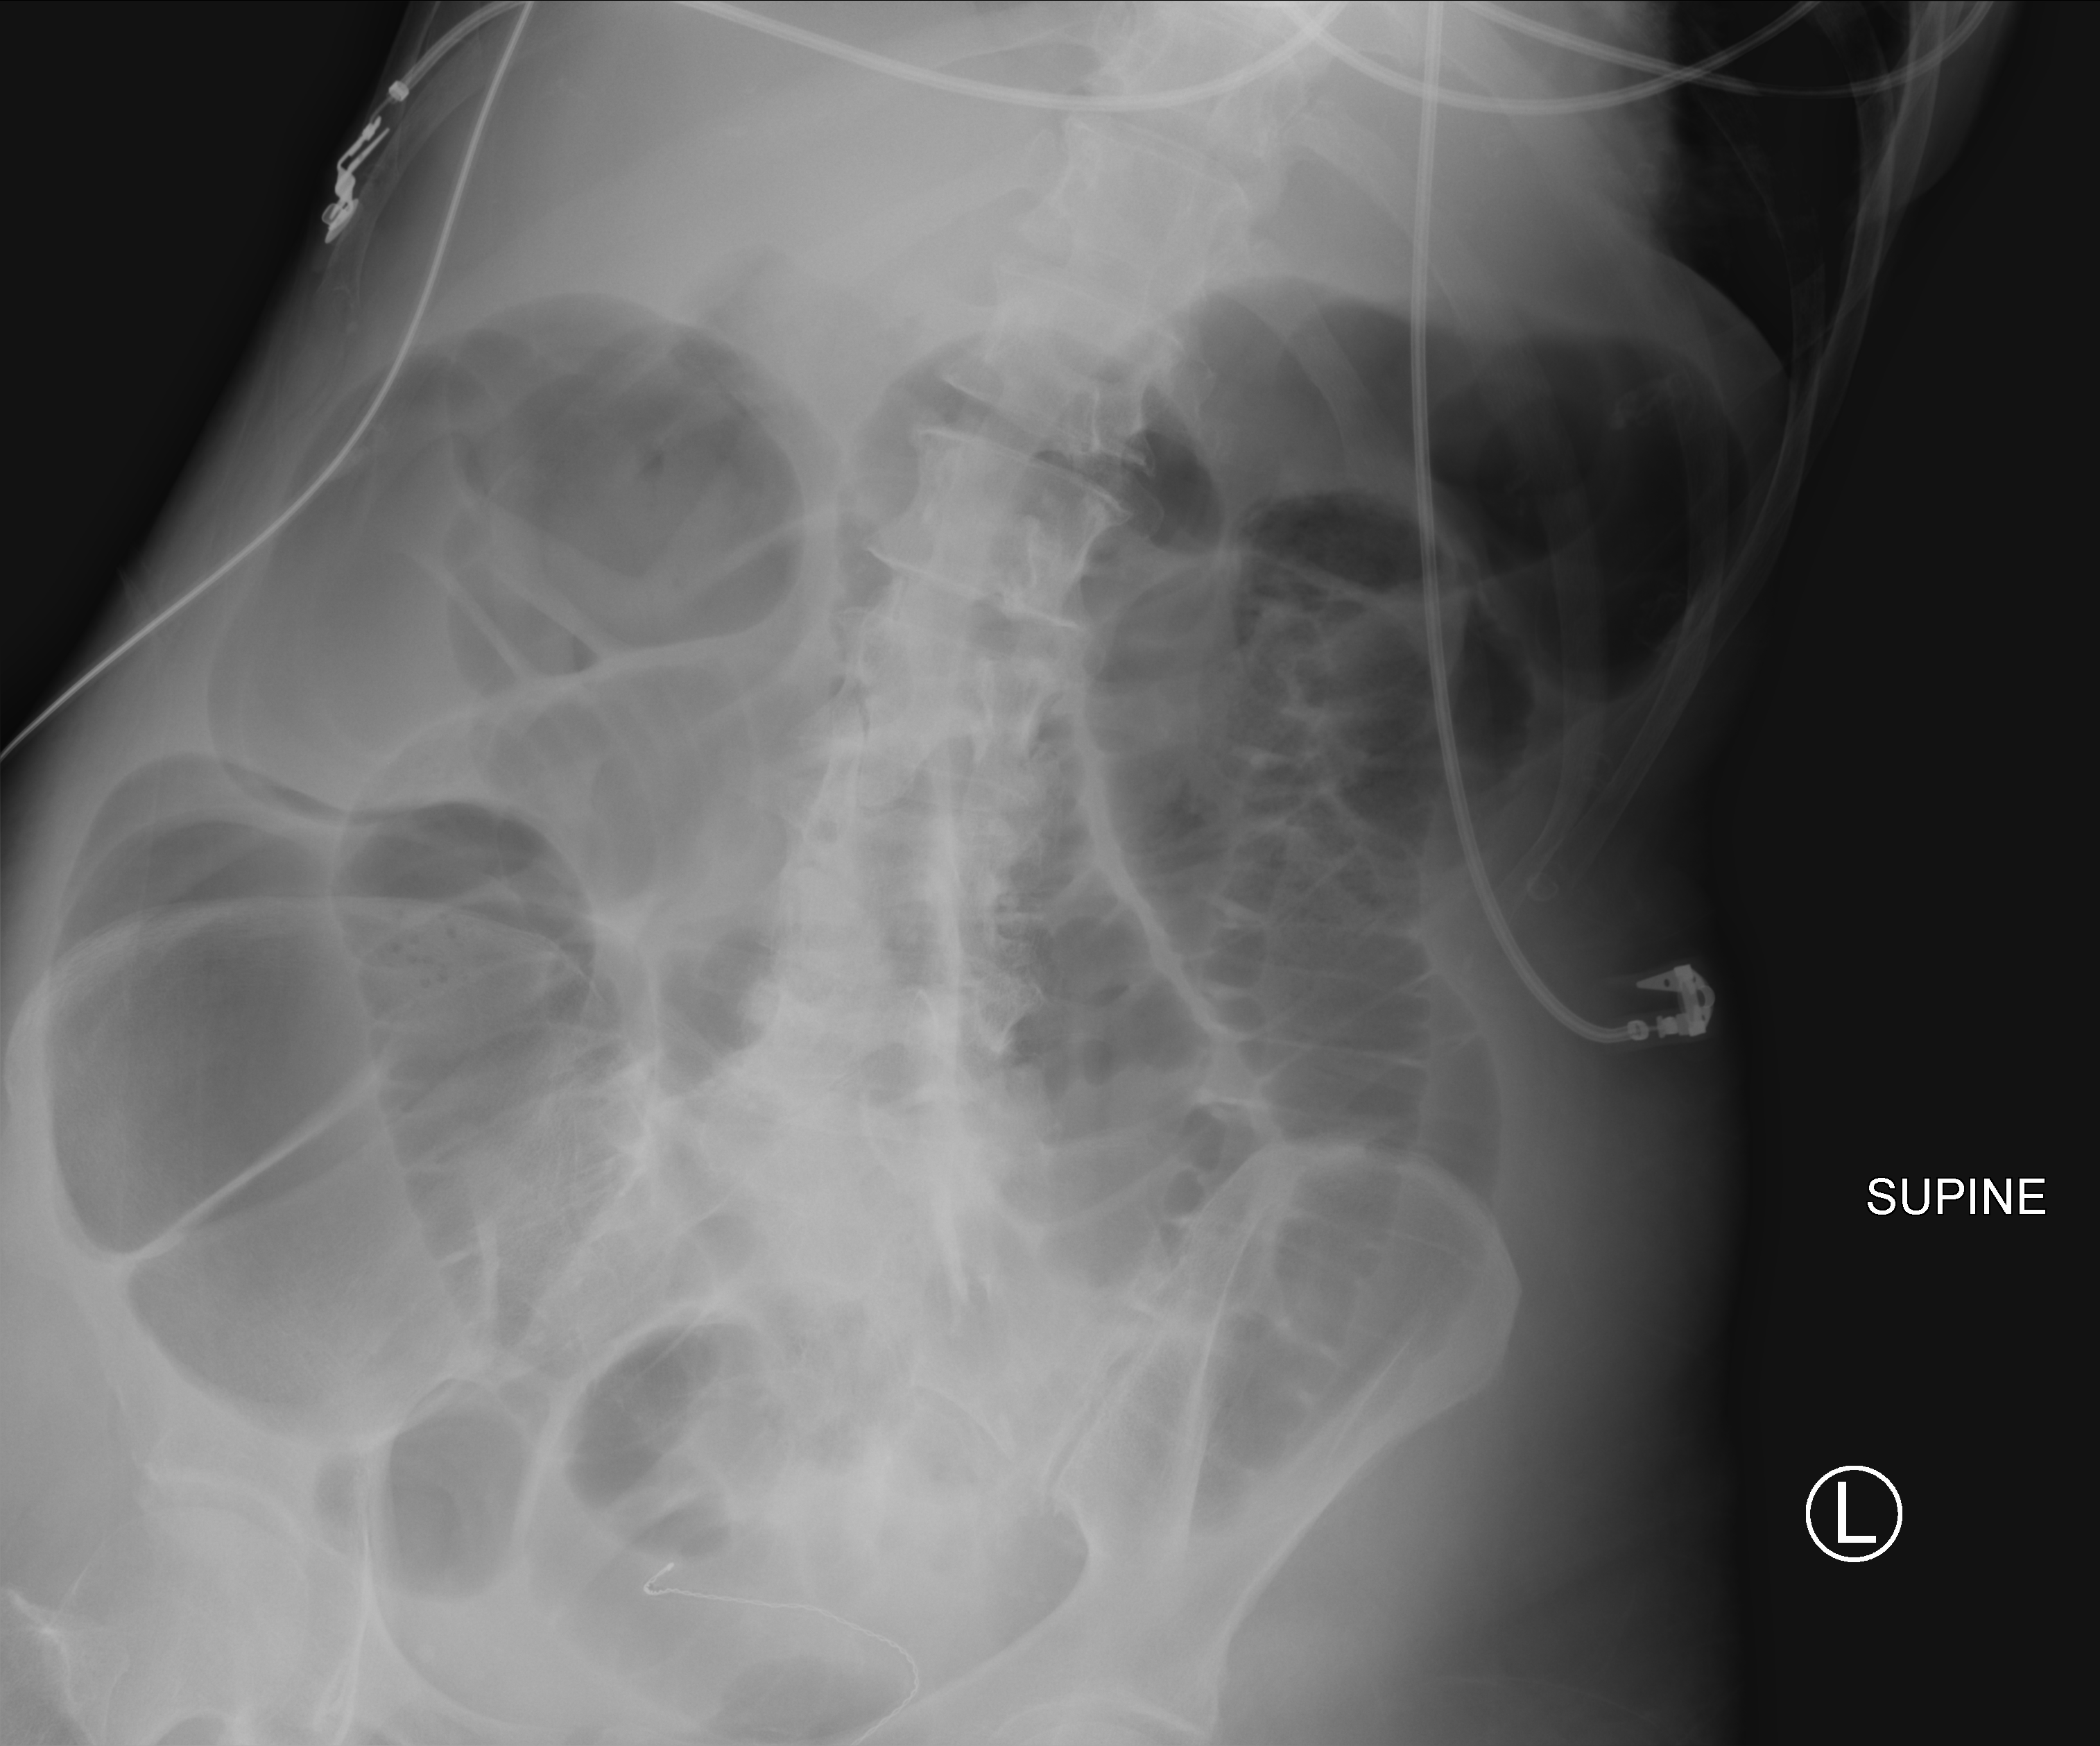
Bedside abdomen radiograph (computed radiography), anteroposterior (AP) projection. Patient hospitalised with COVID-19; female, aged 60–74 years.
Admission-level facts for this patient (not findings on this image; timing relative to this image not recorded): mechanically ventilated during this hospital stay: yes.